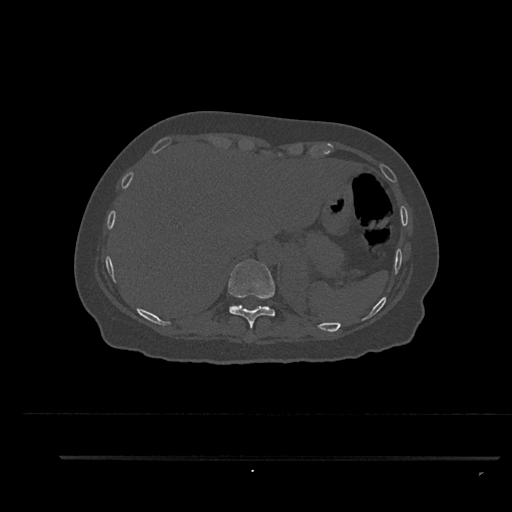
CT including the spine, one axial slice; reconstruction kernel Br40s/3; bone window (W 1800 / L 400 HU); 512 × 512 image matrix, field of view 408 × 408 mm. Patient: female, 44 years. Case-level facts recorded for this patient, not image findings: primary cancer: renal.
Annotated regions visible in this slice (semi-automatically segmented with operator editing):
- T10 vertebra: bounding box <228,259,275,332> (left, top, right, bottom; pixels)